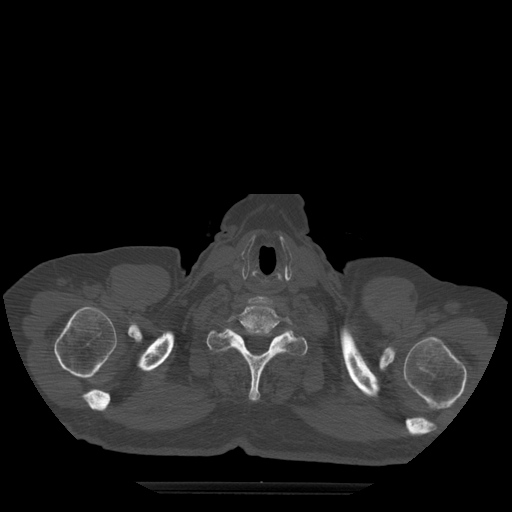
CT including the spine, one axial slice; slice 446 of 522 in the series (ordered by position); bone window (W 1800 / L 400 HU); 1.25 mm slice thickness; 512 × 512 image matrix, field of view 420 × 420 mm. Patient age 72 years. Case-level facts recorded for this patient, not image findings: primary cancer: prostate.
Structures marked on this image (semi-automatically segmented with operator editing):
- T1 vertebra: bounding box (x1, y1, x2, y2) in pixels: (207, 328, 308, 401)